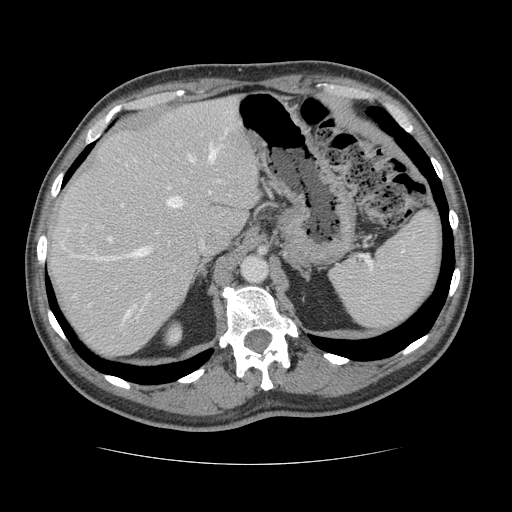
Contrast-enhanced abdominal CT, one axial slice. Position 94 of 134 along the scan axis. Intravenous contrast given. Soft-tissue window (W 400 / L 40 HU). 512 × 512 image matrix, field of view 377 × 377 mm. Male patient, age 68 years. From the clinical record (not read from this slice): diagnosis: colorectal cancer liver metastases, imaged before liver resection; multiple liver metastases: yes; largest metastasis: 2.2 cm; disease in both lobes: no.
Structures marked on this image (expert manual segmentation):
- hepatic veins: bounding box [x1, y1, x2, y2] px = [96, 129, 227, 317]
- liver: [49, 98, 260, 358]
- planned liver remnant (the part of the liver to remain after resection): [49, 98, 260, 333]
- portal vein (with intrahepatic branches): [108, 144, 220, 297]